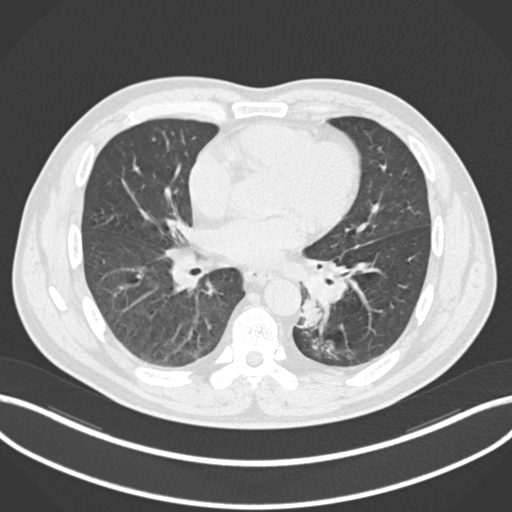
Chest CT, one axial slice; slice 103 of 223 in the series (ordered by position); reconstruction kernel B30f; 120 kVp; lung window (W 1500 / L -600 HU); 1 mm slice thickness; 512 × 512 image matrix. Patient: male, 50 years. Case-level facts recorded for this patient, not image findings: clinical TNM (as recorded): T2a N3 M0.
Annotated regions visible in this slice (bounding box drawn by a radiologist):
- lung tumour (recorded histology: squamous cell carcinoma): box from (x=299, y=293) to (x=326, y=334) px